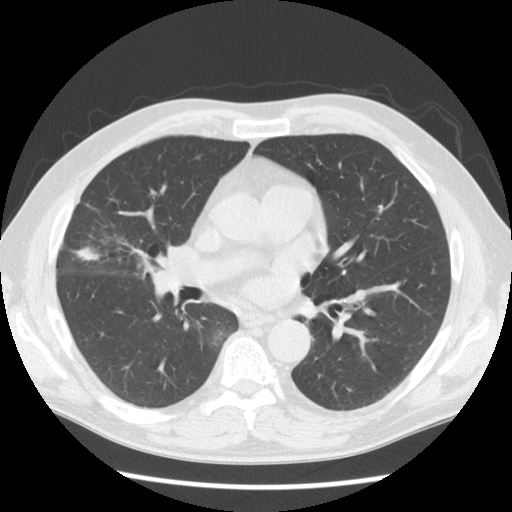
Low-dose screening chest CT, one axial slice; position 80 of 146 along the scan axis; reconstruction kernel STANDARD; lung window (W 1500 / L -600 HU); 2.5 mm slice thickness; 512 × 512 image matrix, field of view 350 × 350 mm.
Structures marked on this image (outlined manually by an expert reader):
- lesion 1 (tumor, middle lobe of right lung): bounding box [x1, y1, x2, y2] px = [73, 248, 100, 261]